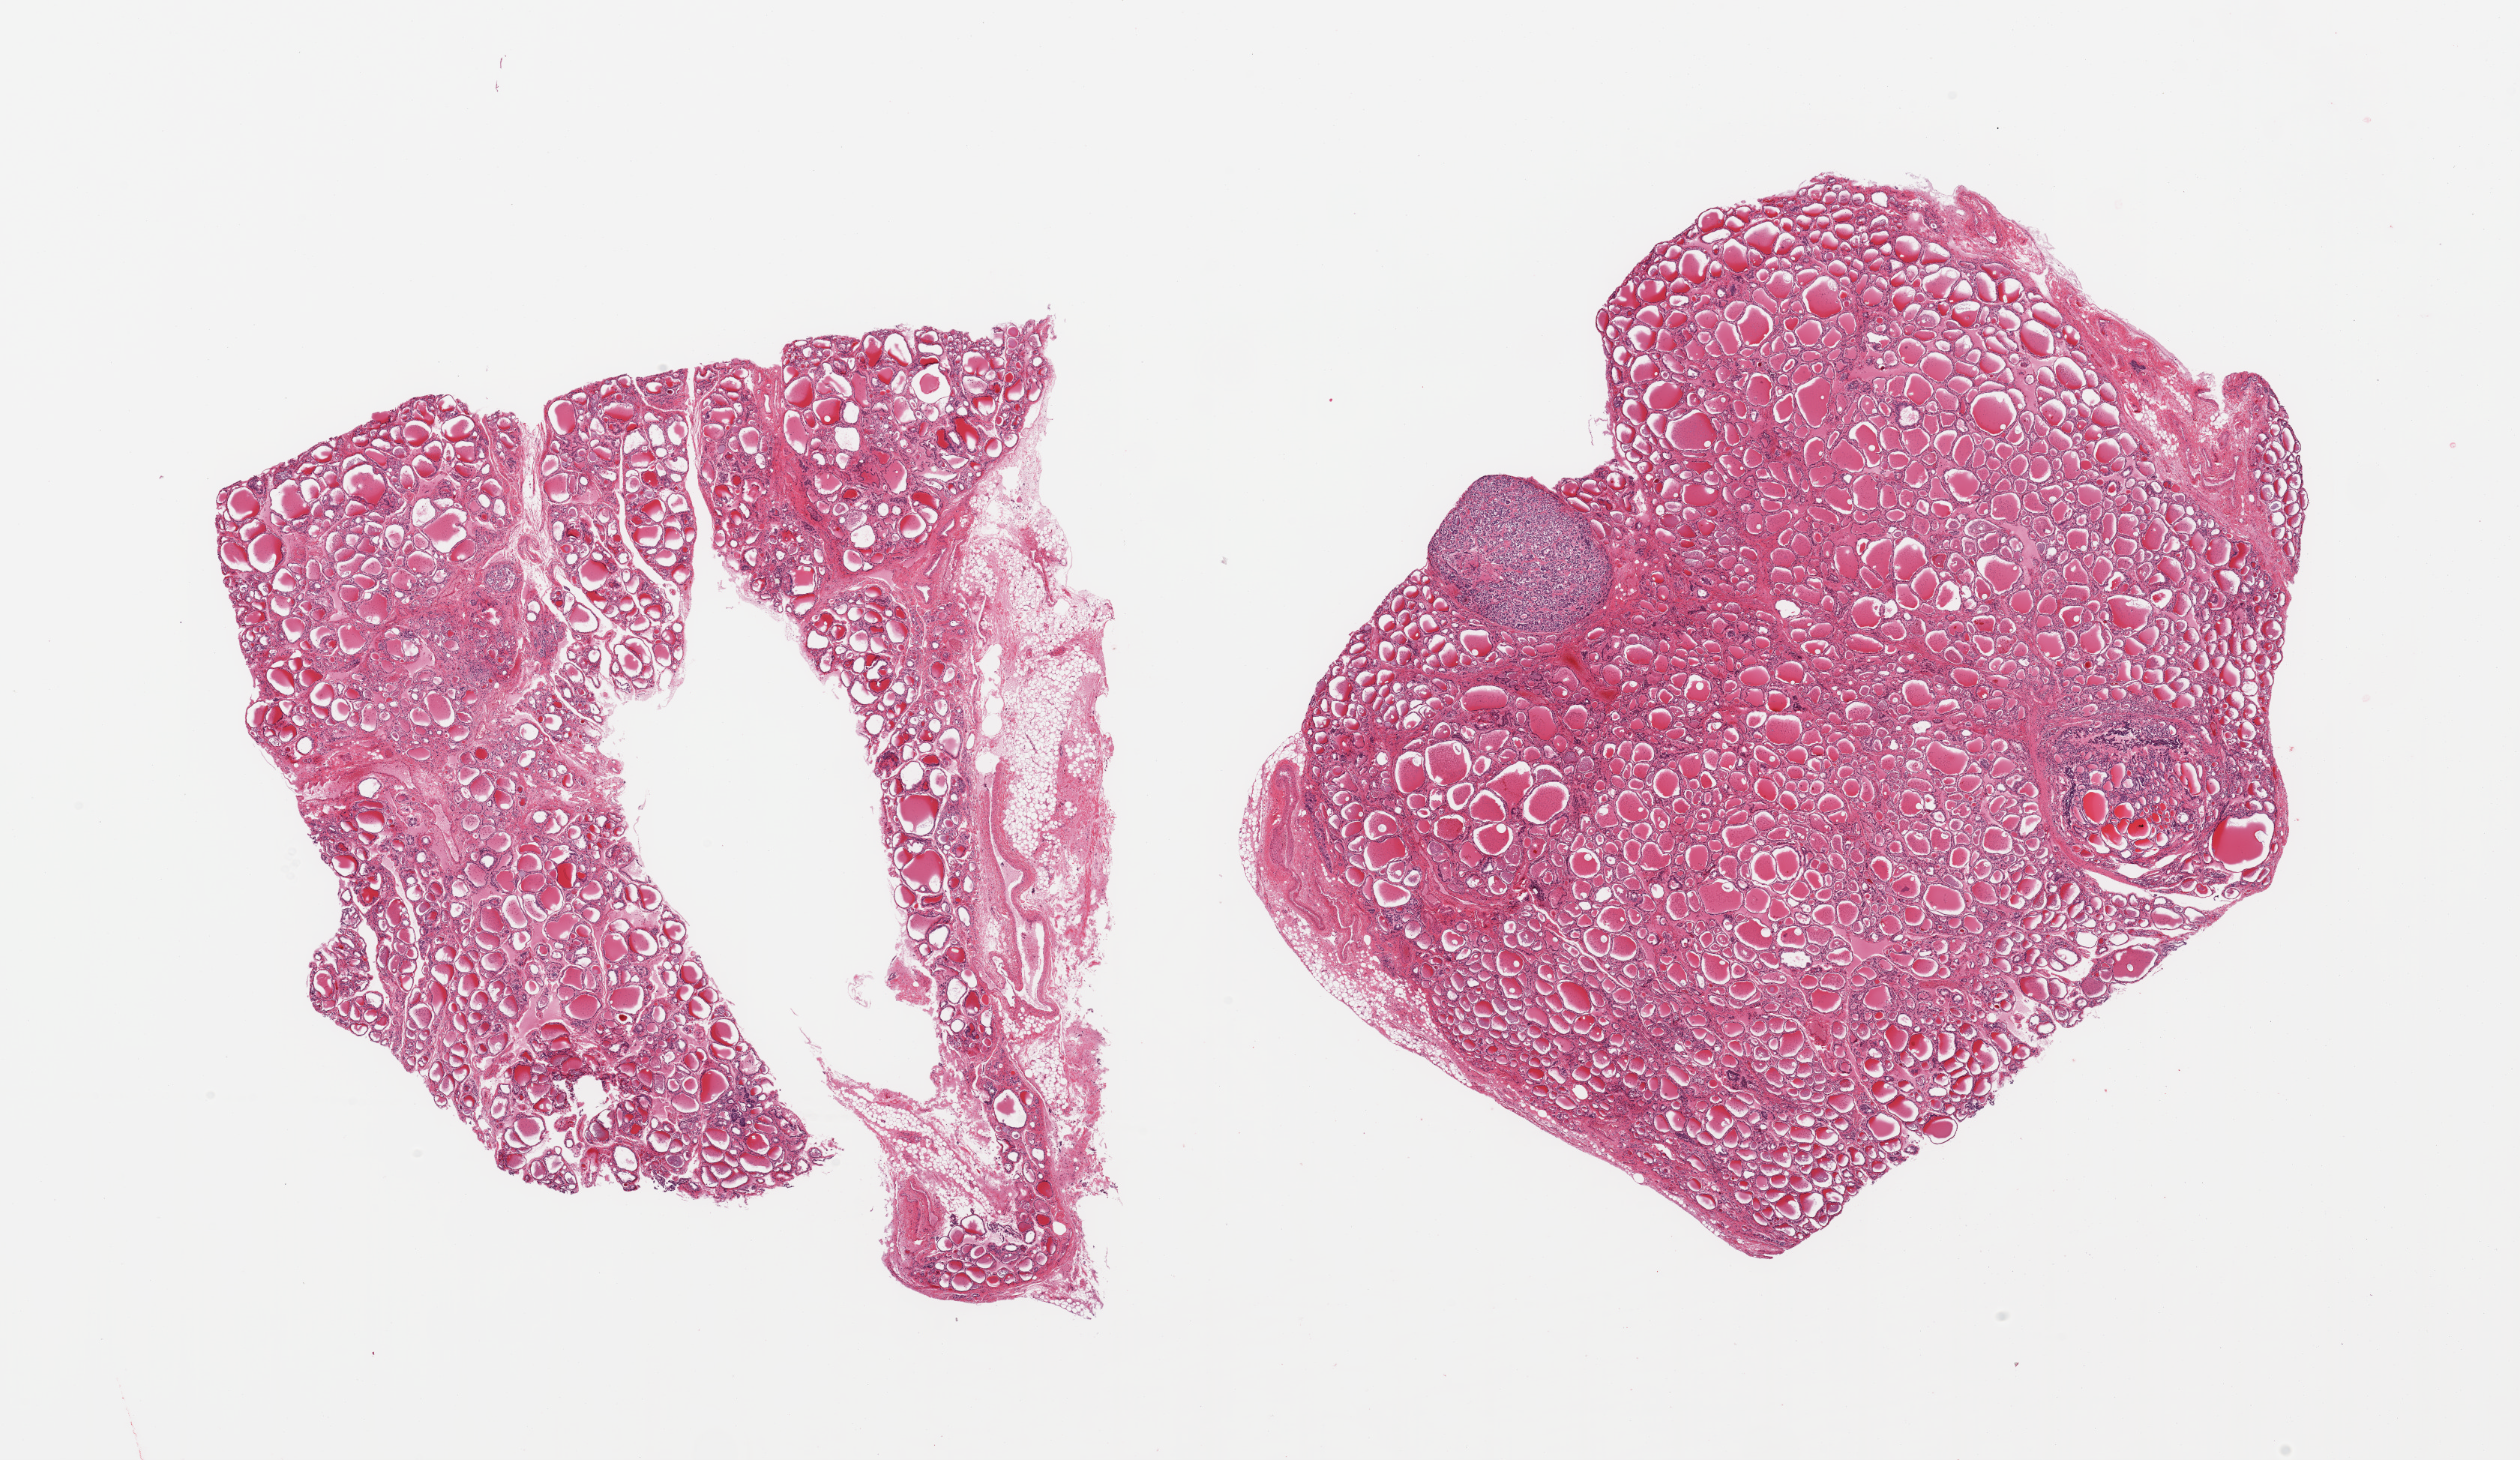
Digitized haematoxylin and eosin-stained section — low-resolution overview of the scanned area, about 26.6 x 15.4 mm (acquisition: 20x scan), PAXgene-fixed paraffin-embedded (PFPE) section, sampled site (target tissue): thyroid, tissue donor sample. Male donor.
* pathologist's review note for this sample: 2 pieces; 2 adenomatoid nodules <2mm